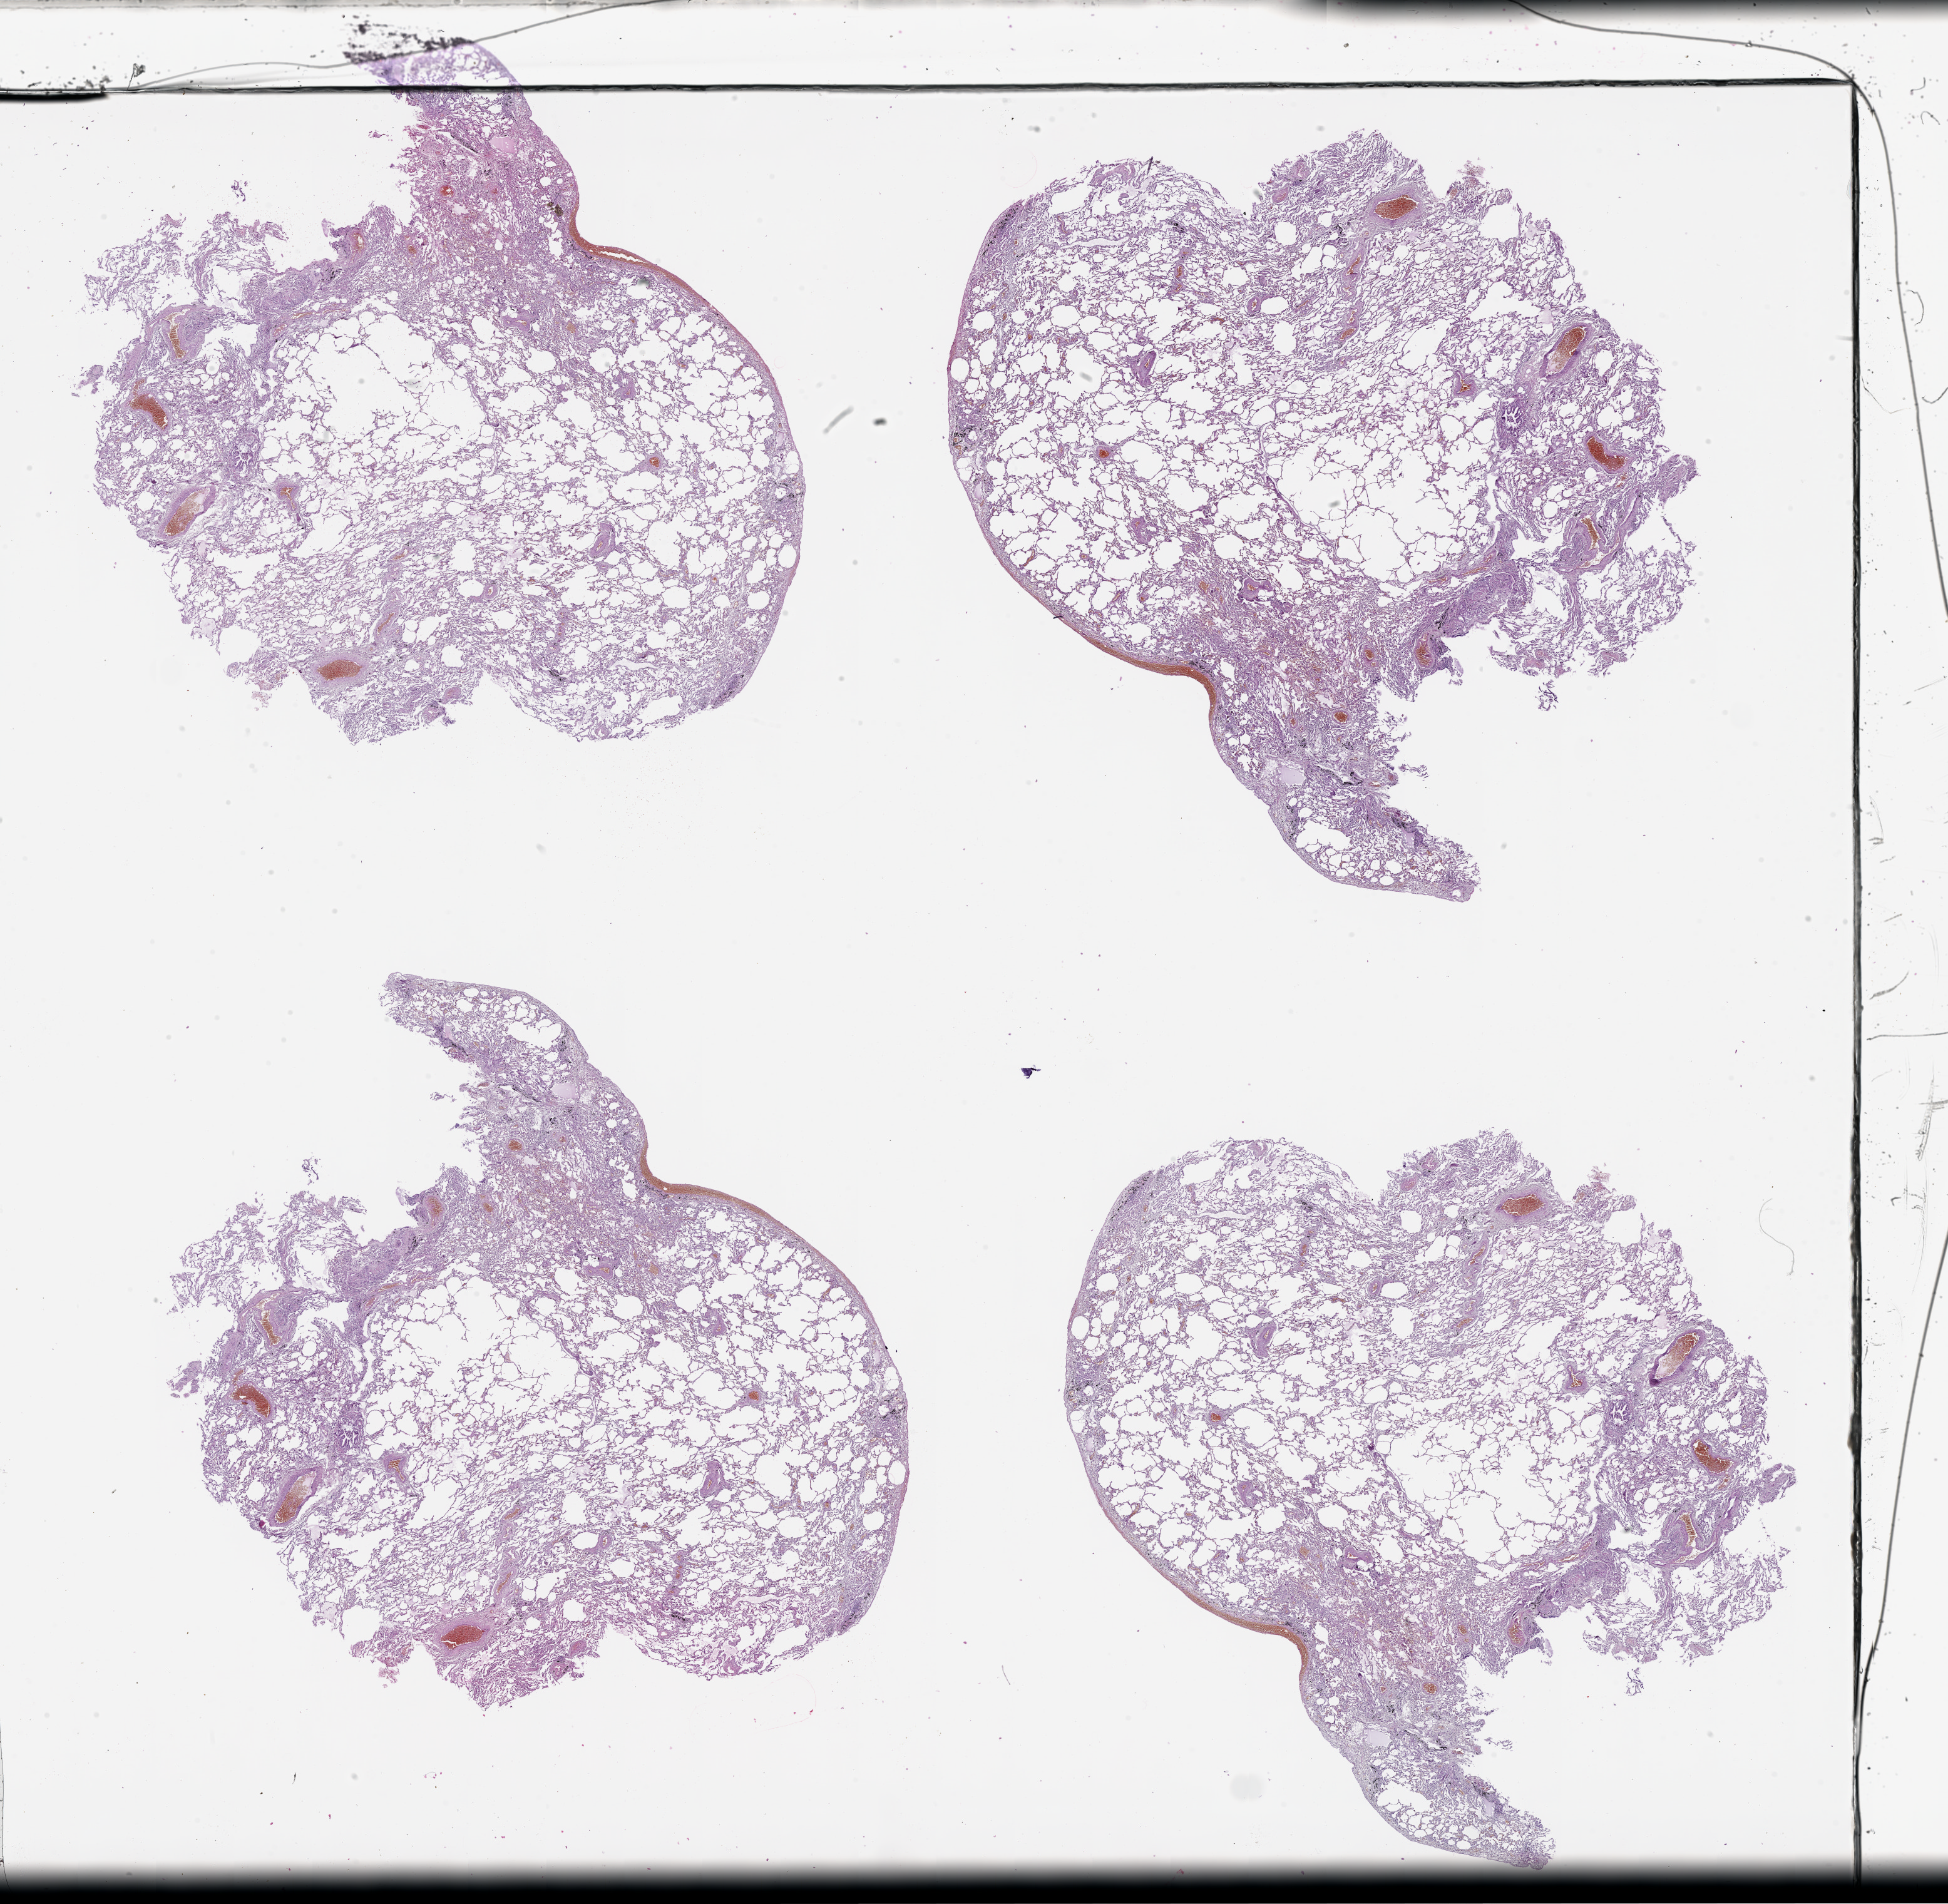
Digitized H&E-stained tissue section (whole slide), shown as a low-resolution overview of the whole scanned area (about 25.1 x 24.5 mm, from a 20x scan); normal (non-tumour) tissue sample, sampled site: lung. Patient: male, age 61 years.
* this section: normal (non-tumour) tissue from the same patient
* patient diagnosis: Adenocarcinoma, NOS